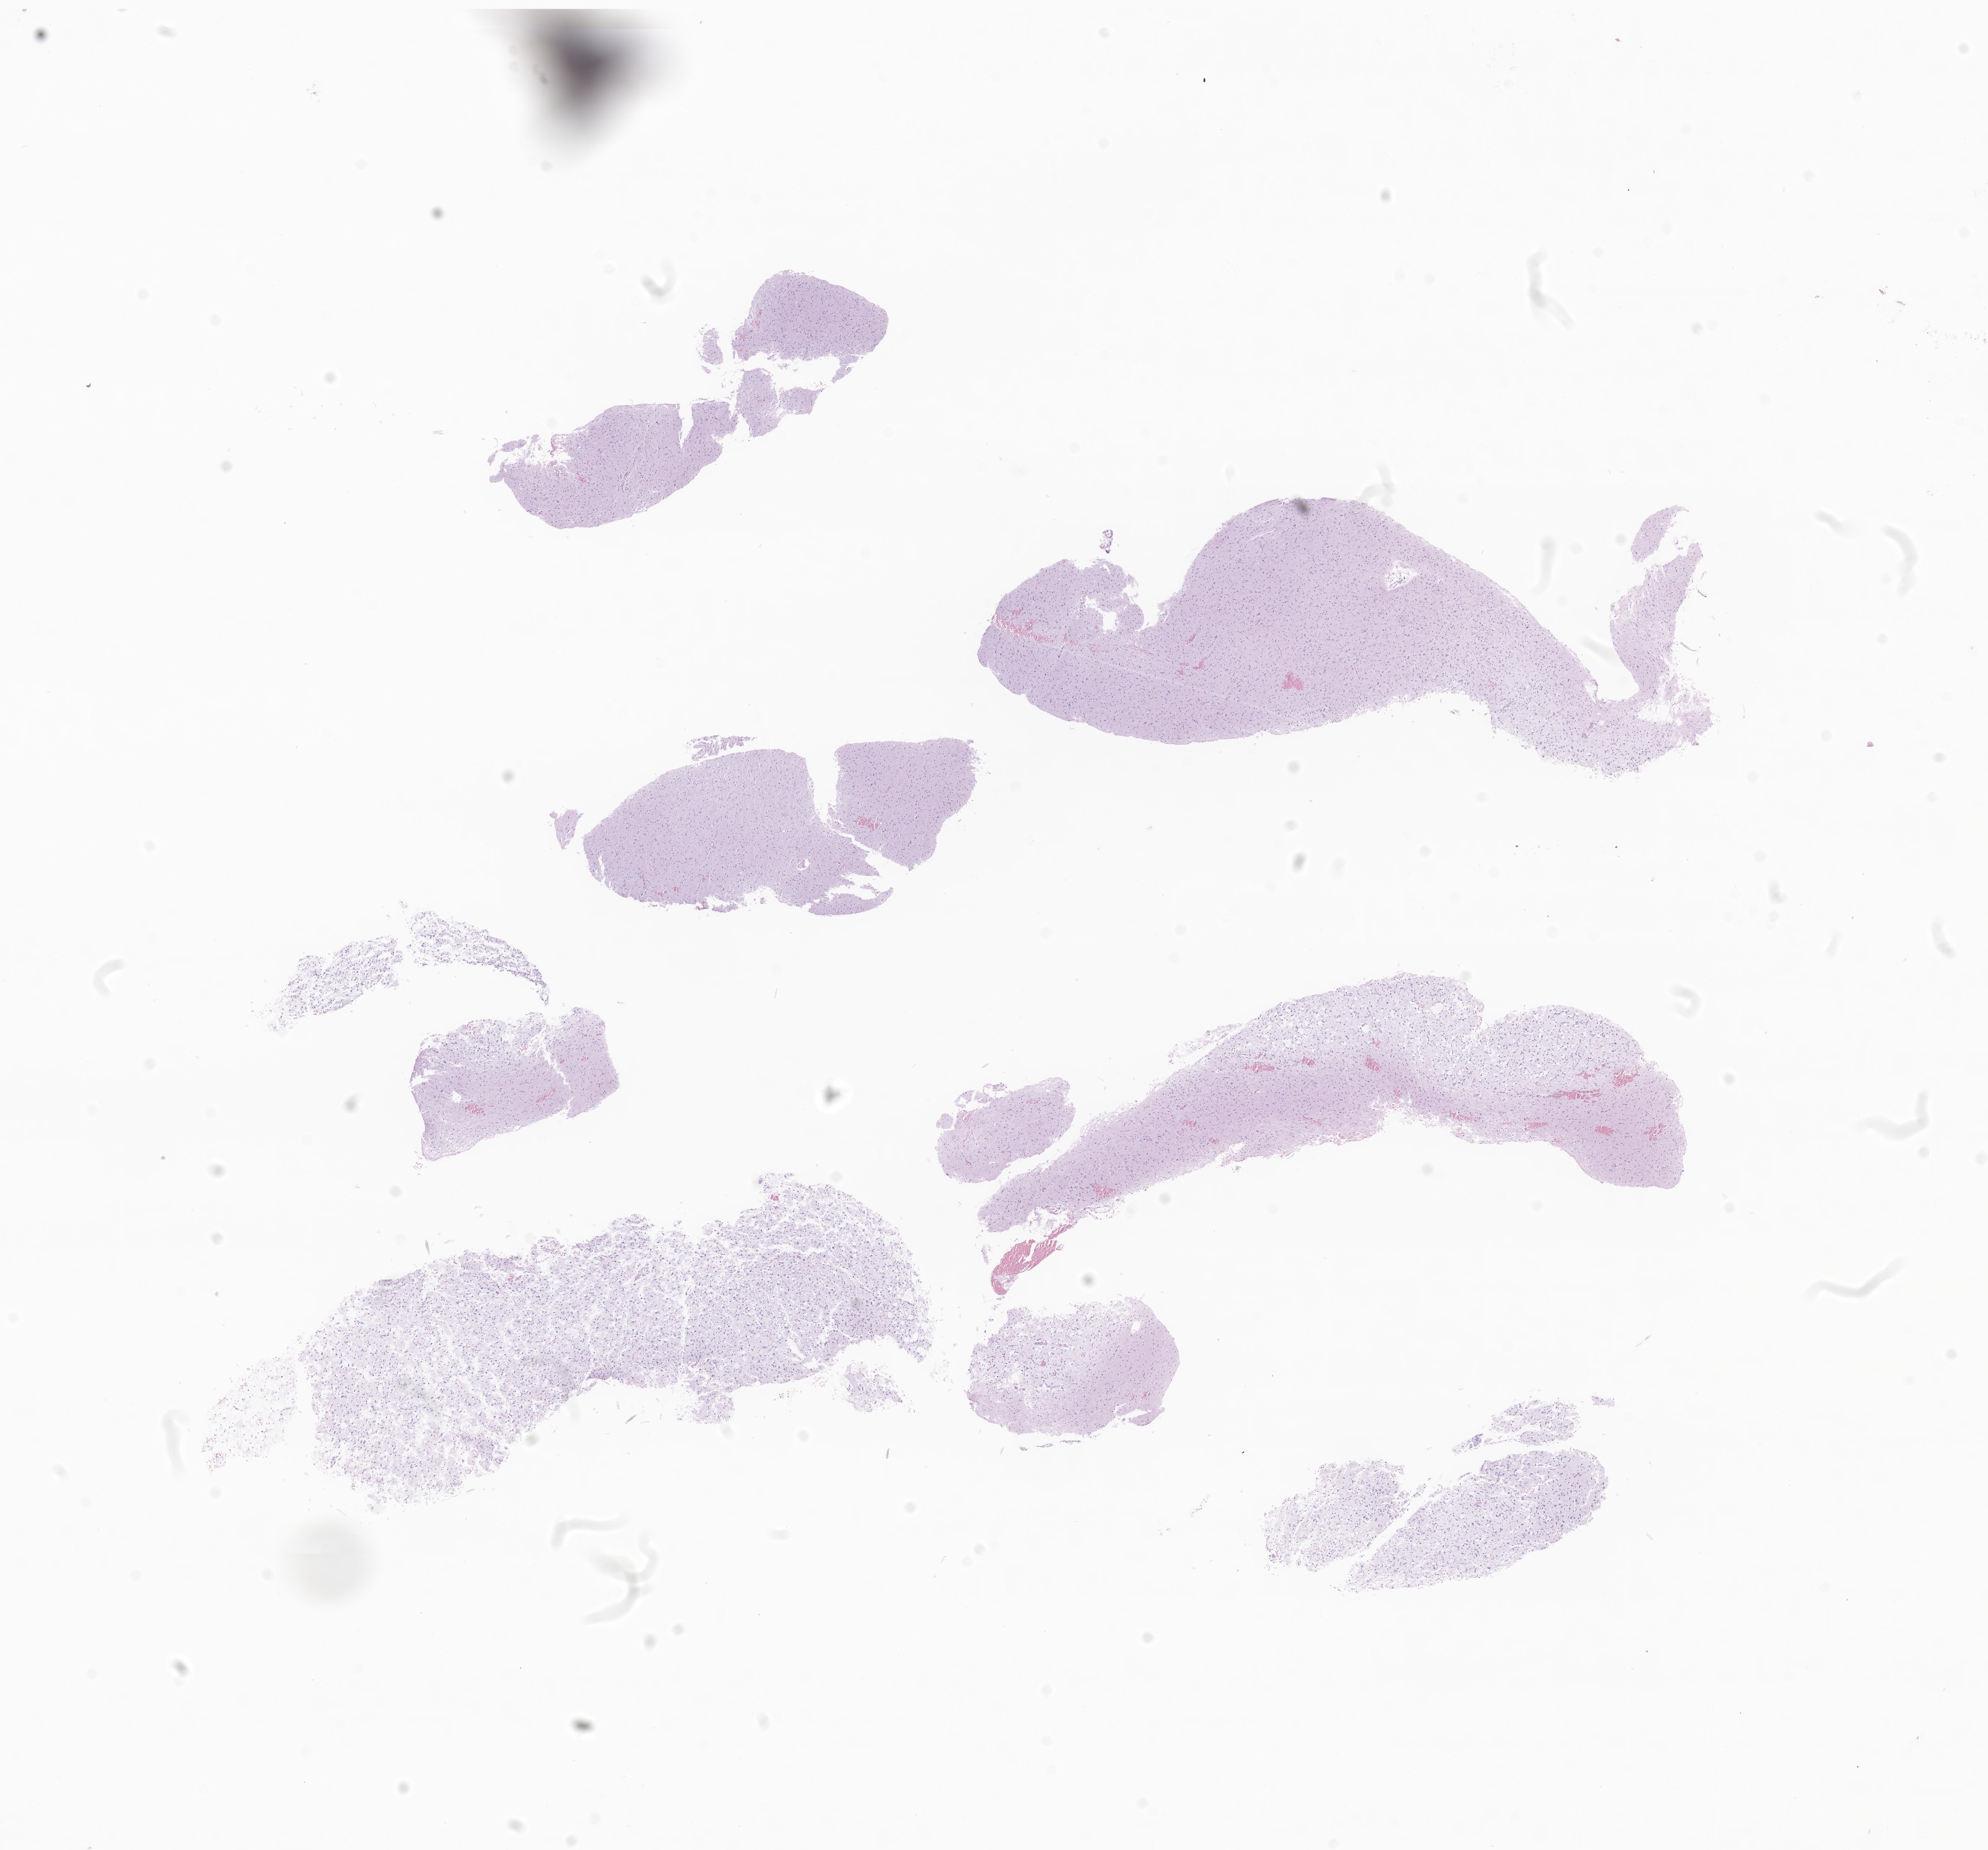
Hematoxylin and eosin (H&E) whole-slide image of tumor tissue from the frontal lobe — shown as a low-resolution overview of the whole scanned area (about 13.9 x 13.0 mm). FFPE section. Patient male; age 145 months.
Diagnosis: Oligoastrocytoma, NOS.